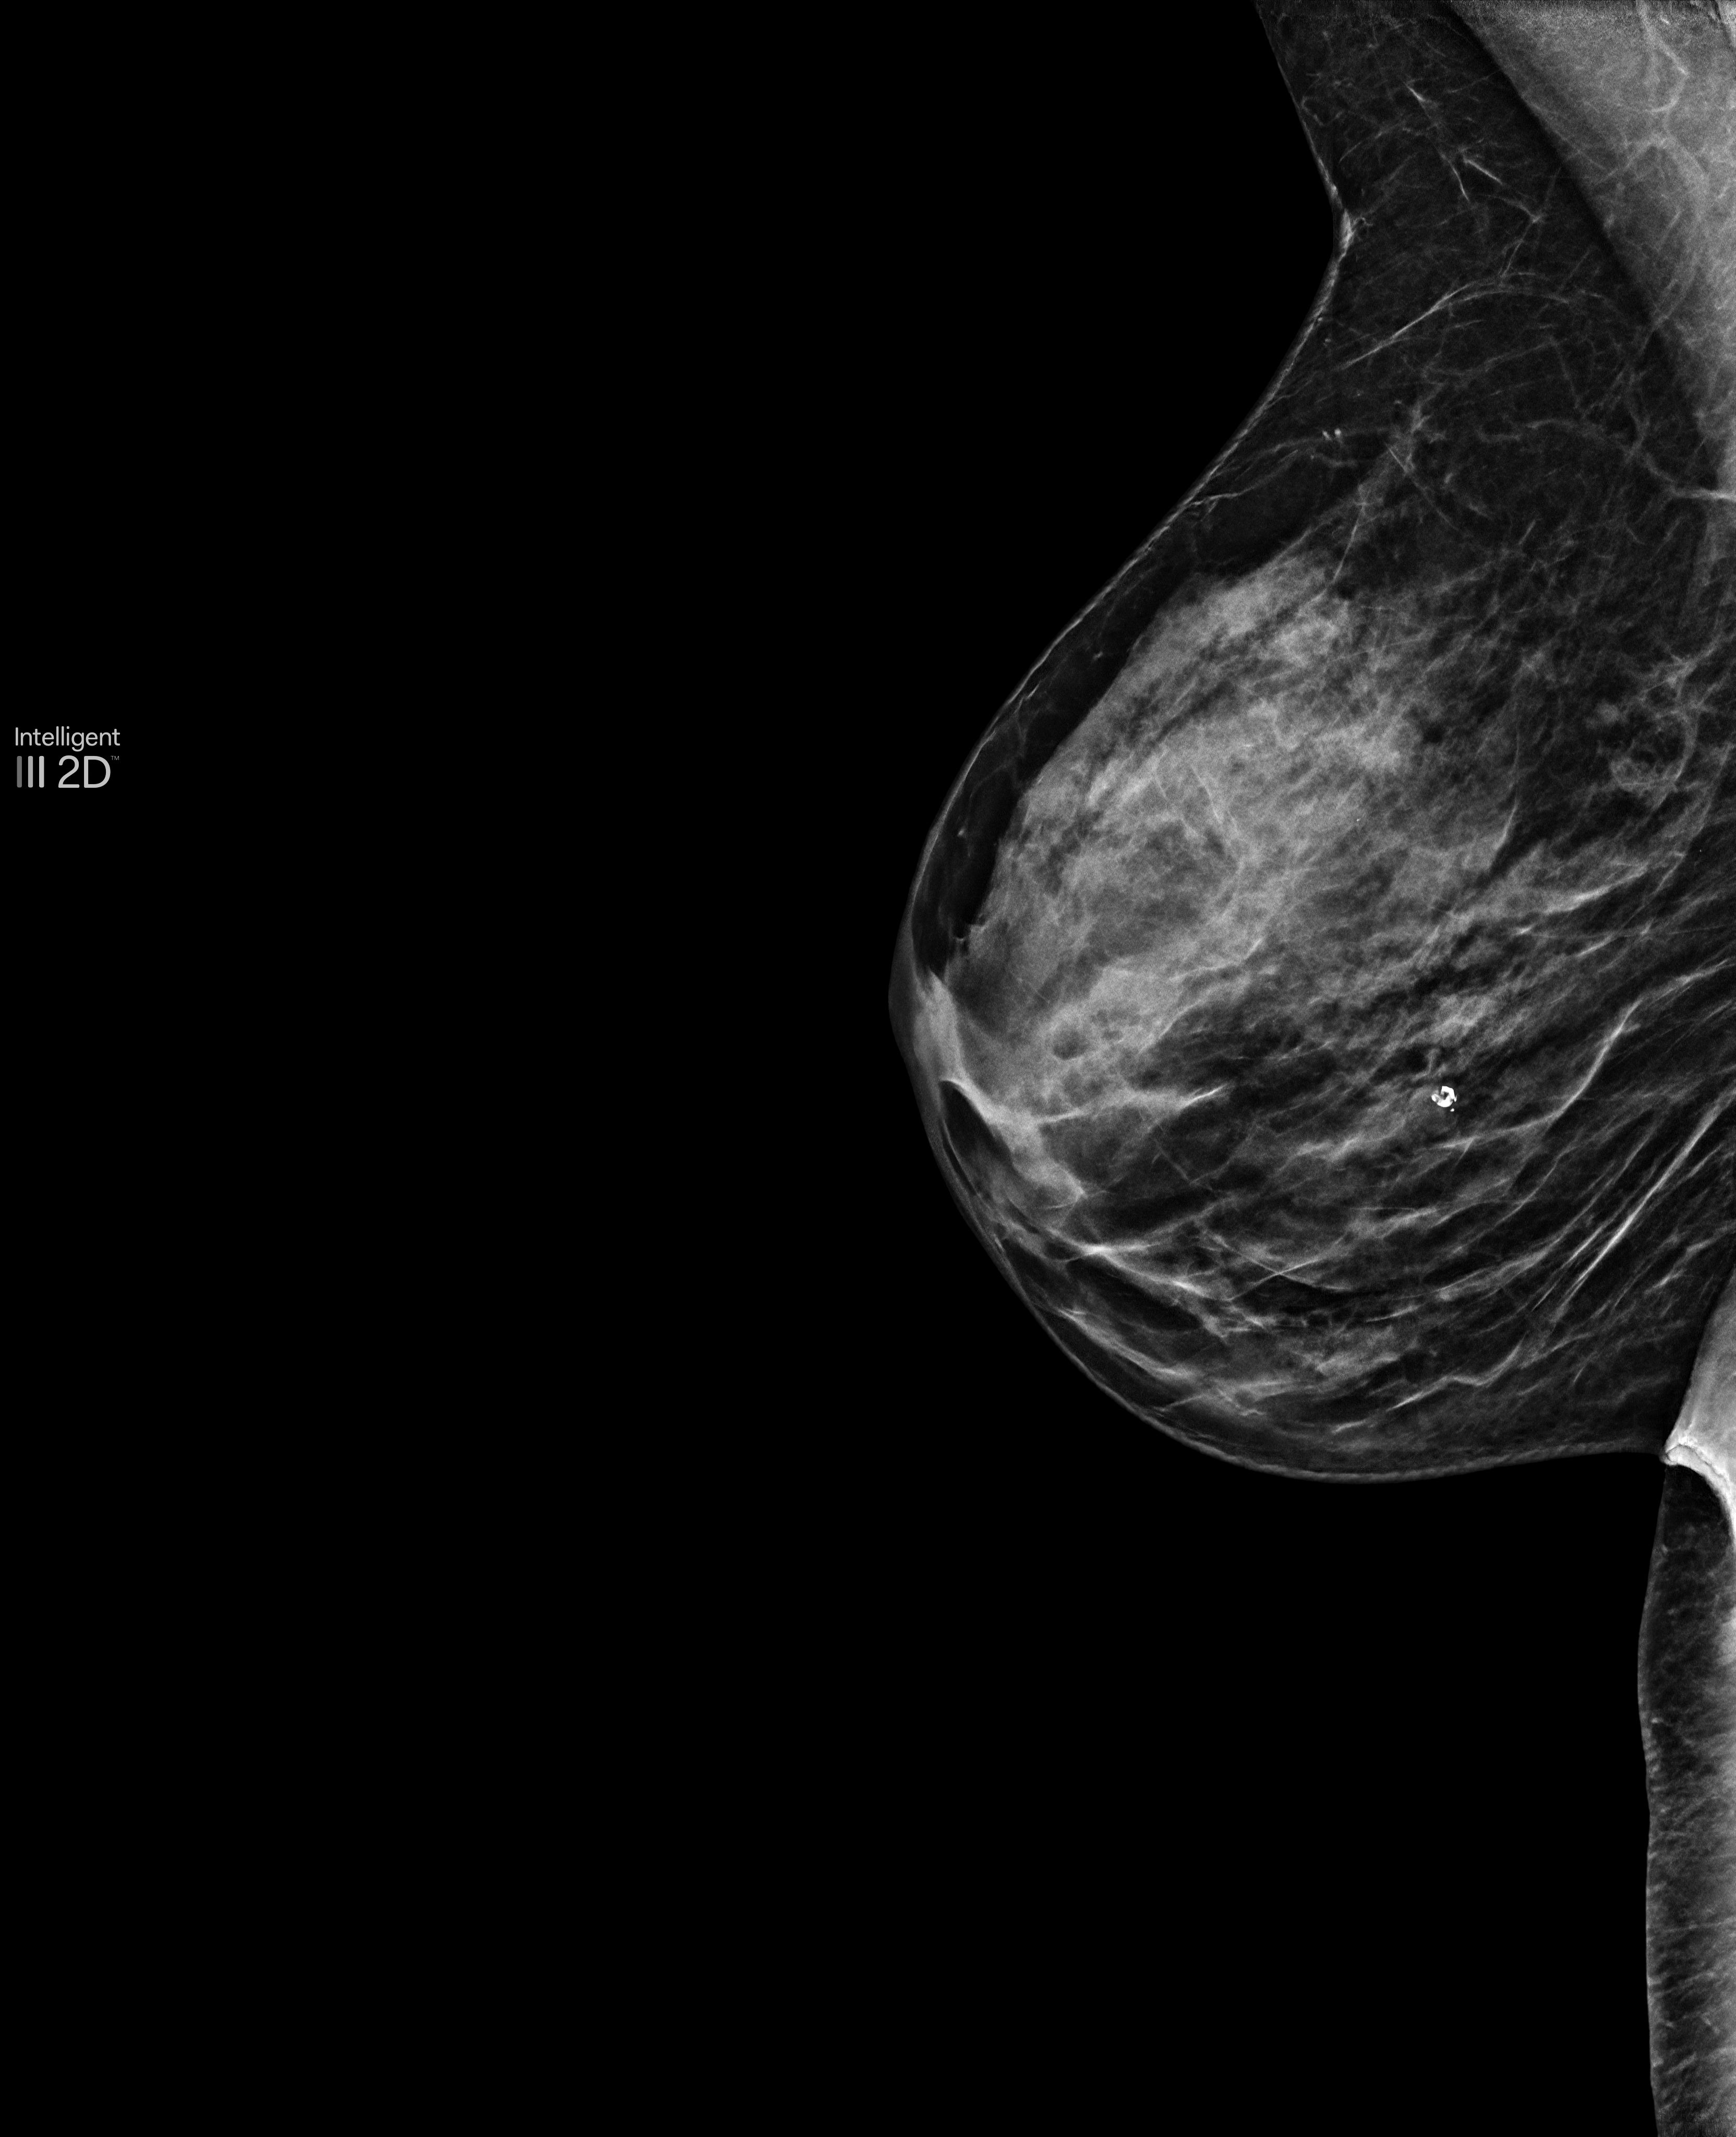
Screening examination; compressed breast thickness 44 mm. Patient: female, 51 years.
Image type: synthesized 2-D view from tomosynthesis. Breast: right. Projection: medio-lateral oblique projection.